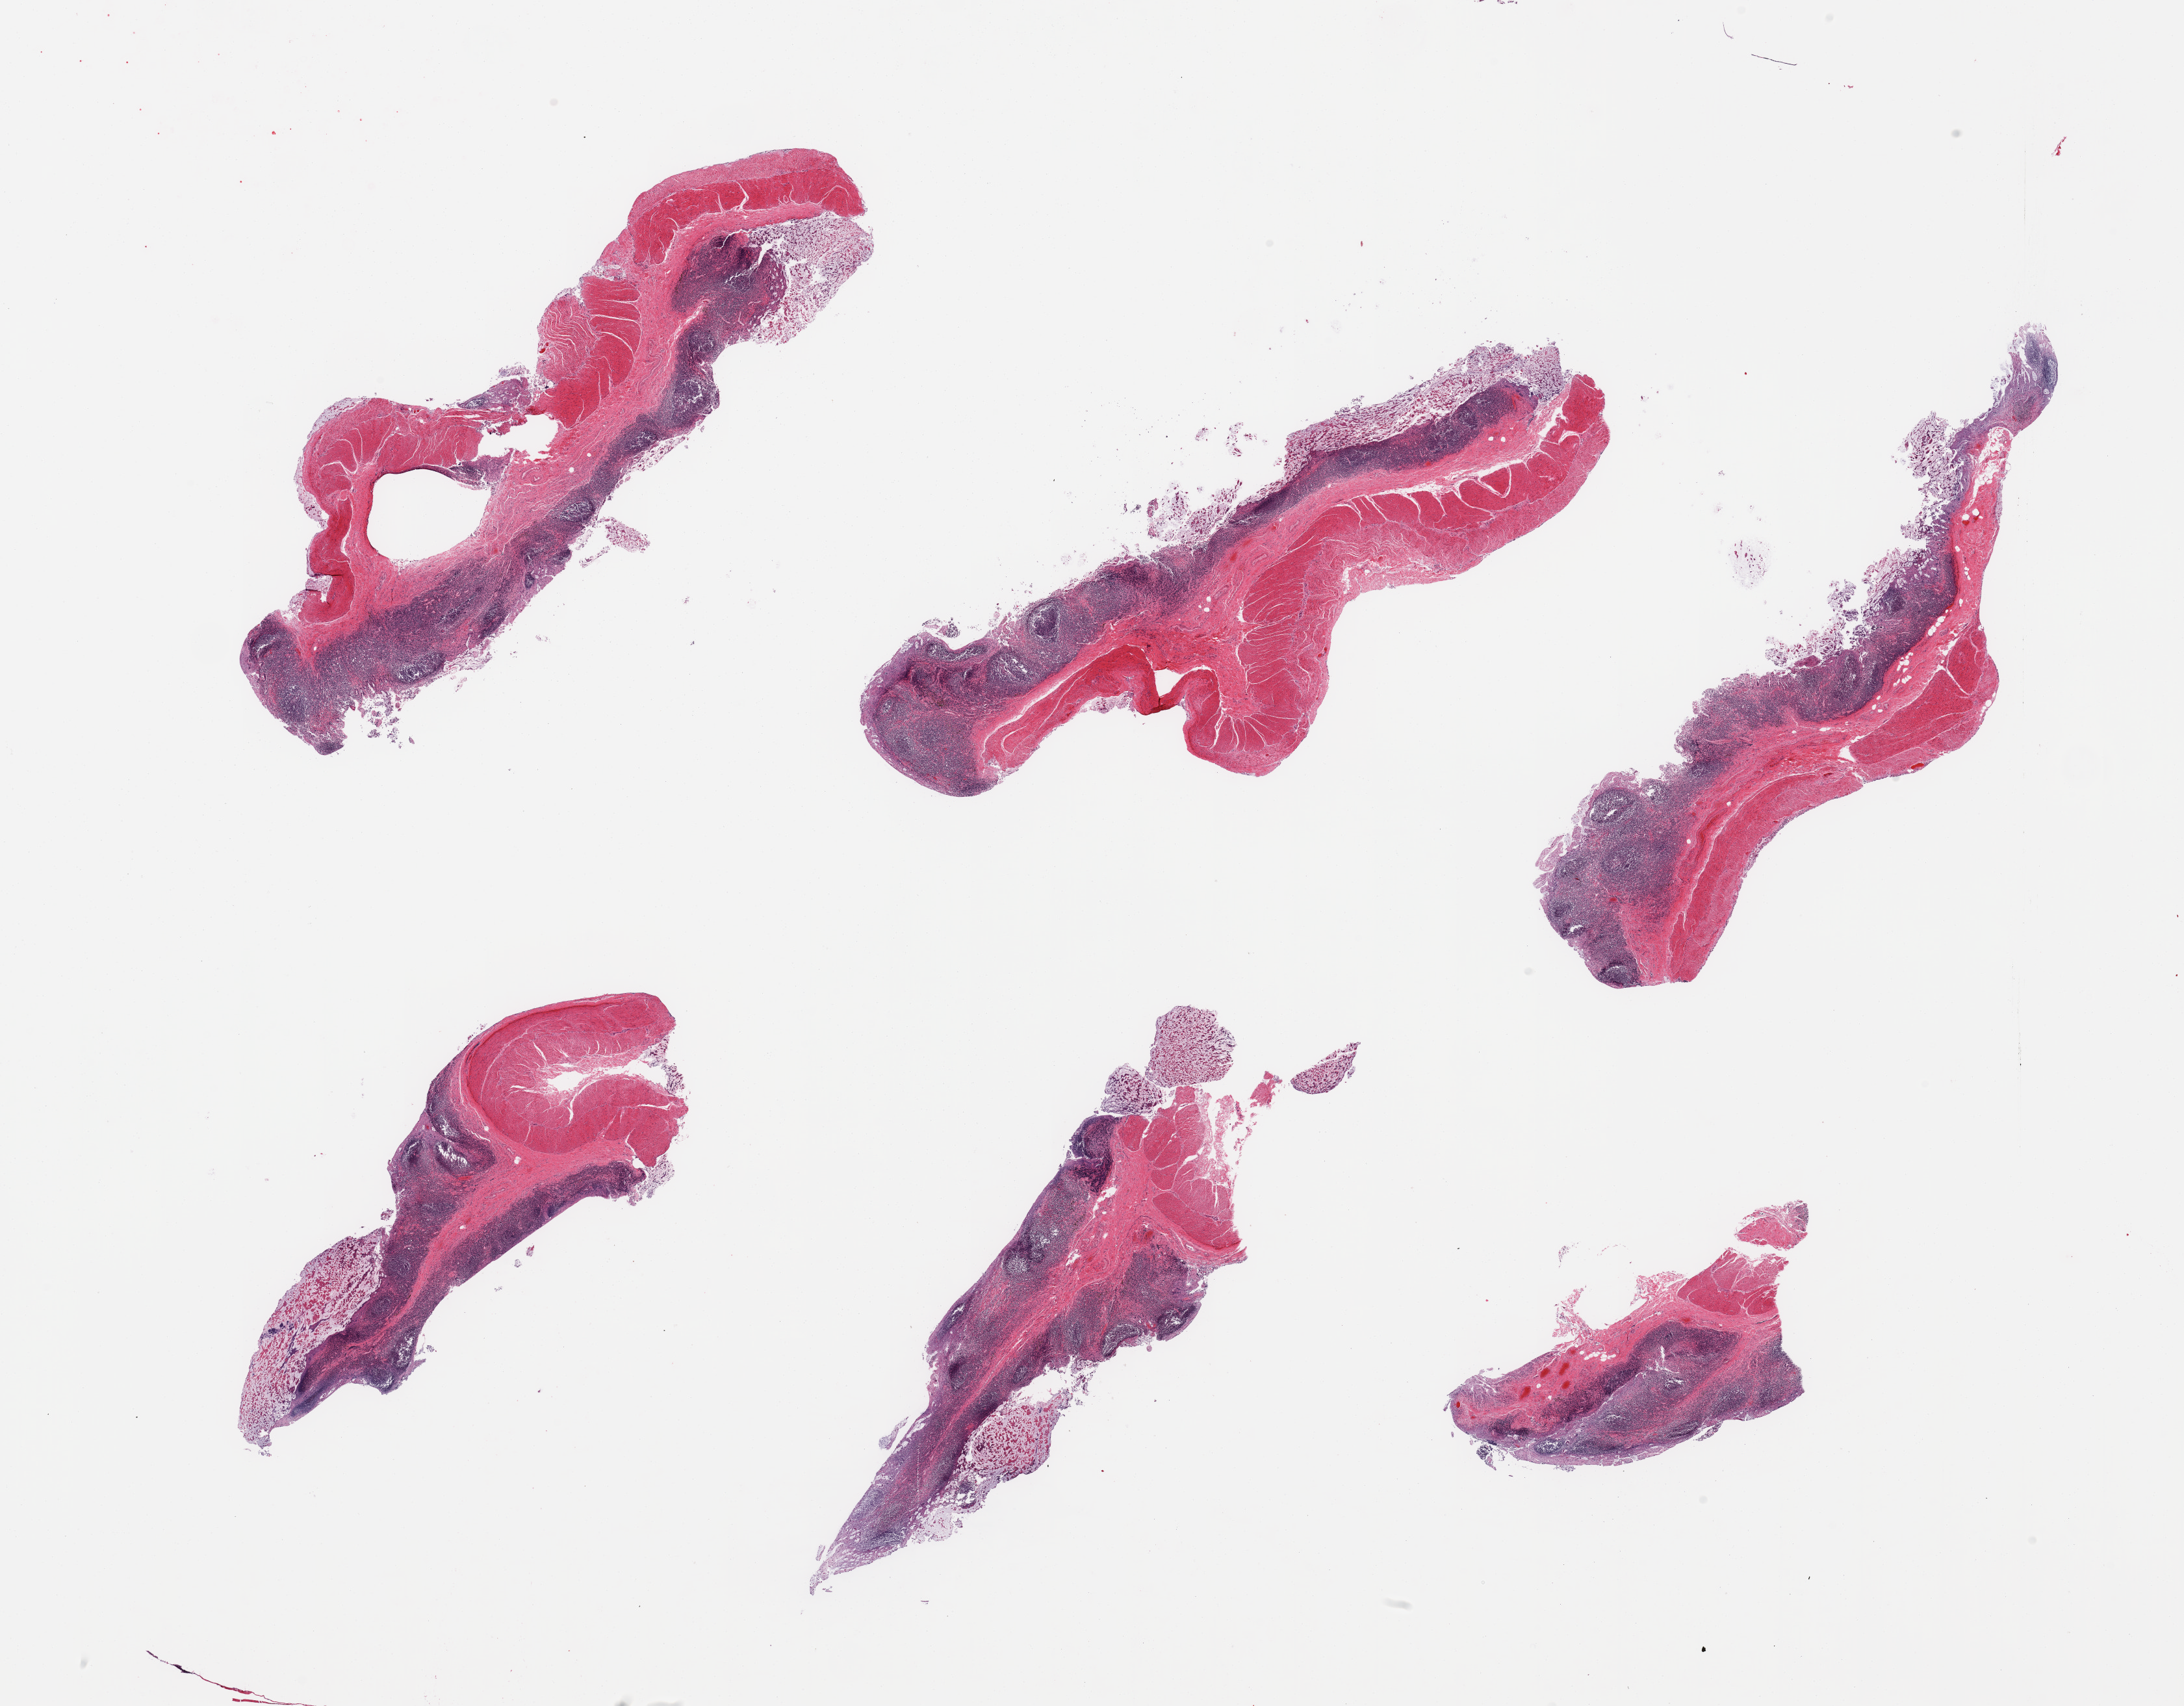
Whole-slide image, hematoxylin and eosin (H&E) stain, brightfield — whole scanned area (about 26.6 x 20.8 mm, from a 20x scan) shown as a low-resolution overview.
Specimen: PAXgene-fixed, paraffin-embedded tissue; section of ileum (target tissue); tissue donor sample.